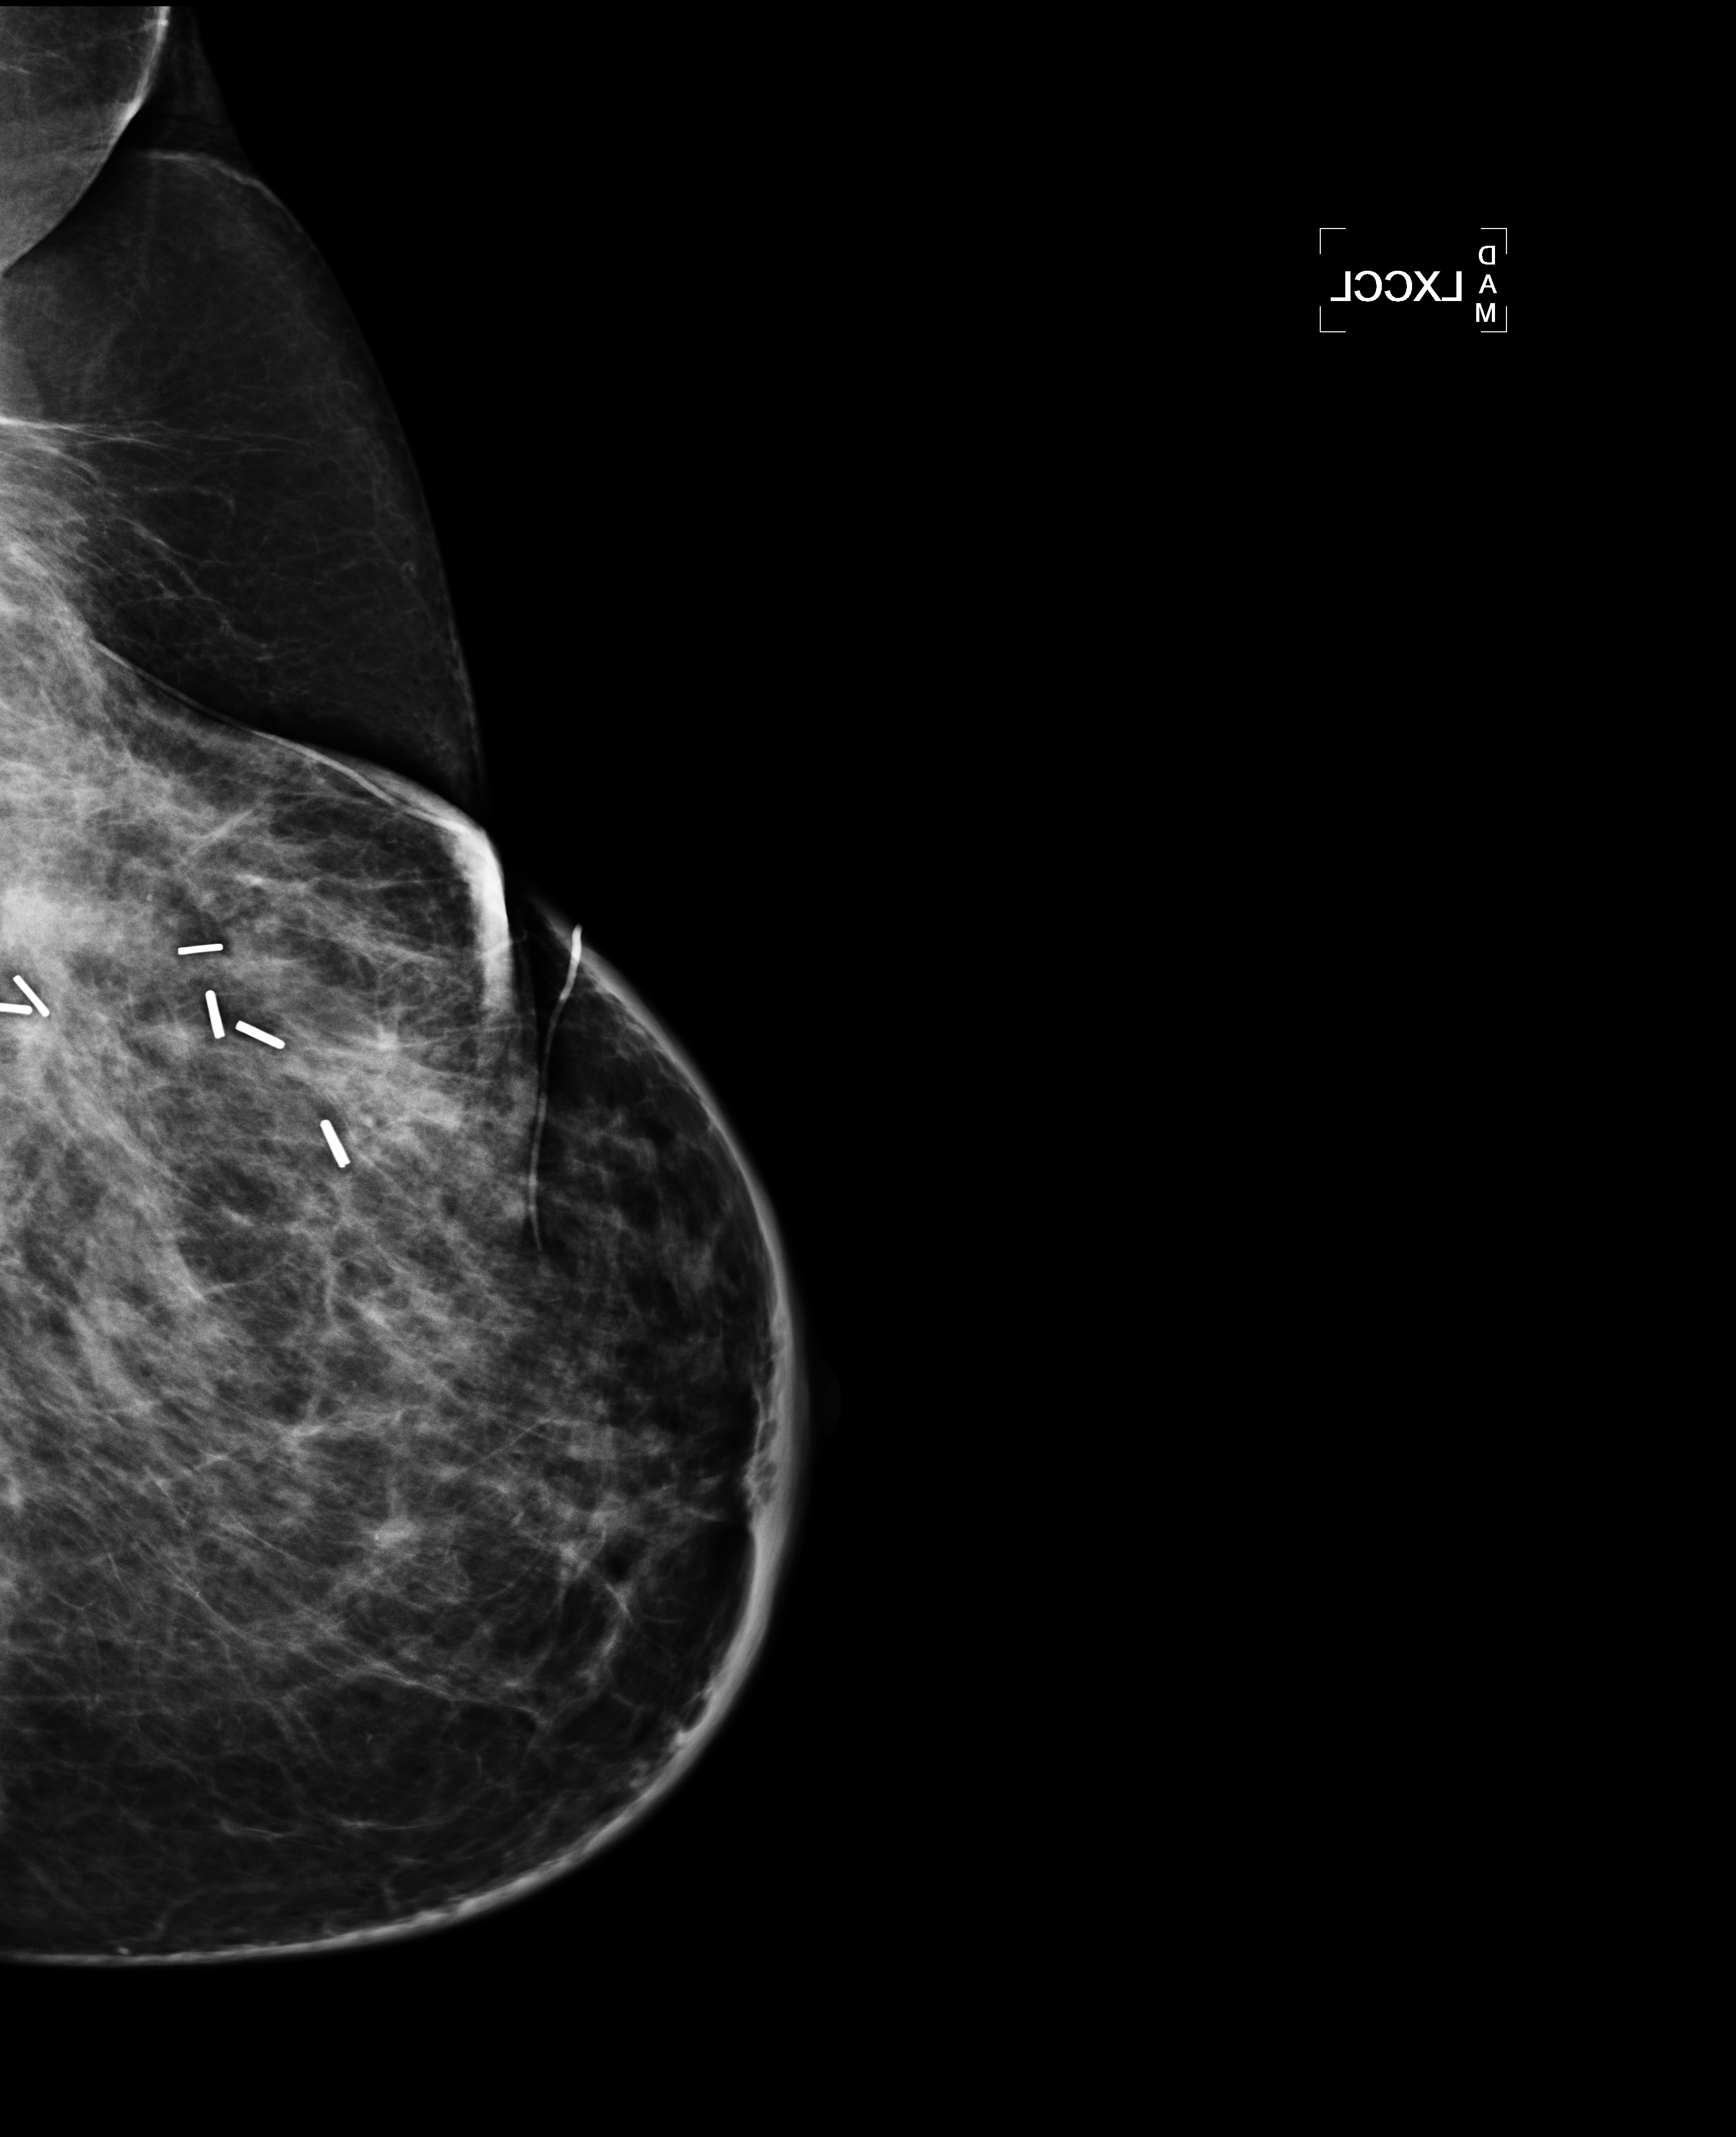
Mammogram, left breast, XCCL view; patient in her 50s.
Patient-level pathology facts (clinical record, not image findings): pathology diagnosis: Invasive ductal CA (left breast); receptor status (as recorded): ER pos, PR pos (weak), HER2 neg; Ki-67 (as recorded): intermed prolif; pathology report notes: re-bx [date] was scar tissue from RT rx.